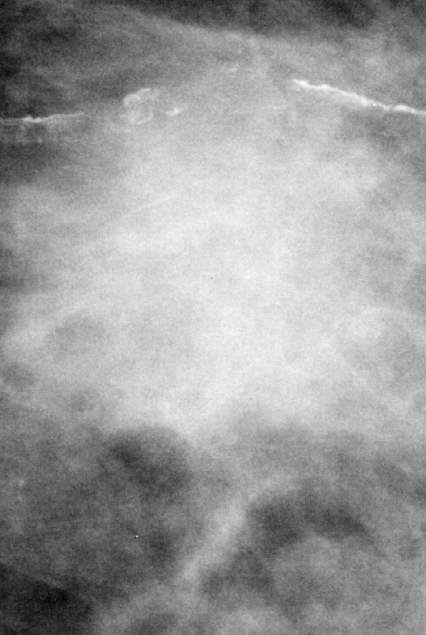
Crop from a digitized film mammogram around one marked abnormality, right breast, CC view, BI-RADS breast density category 2 (scale 1–4).
Finding: mass, shape round, margins ill defined; BI-RADS assessment category 5; pathology result (as recorded, not read from the image): malignant.